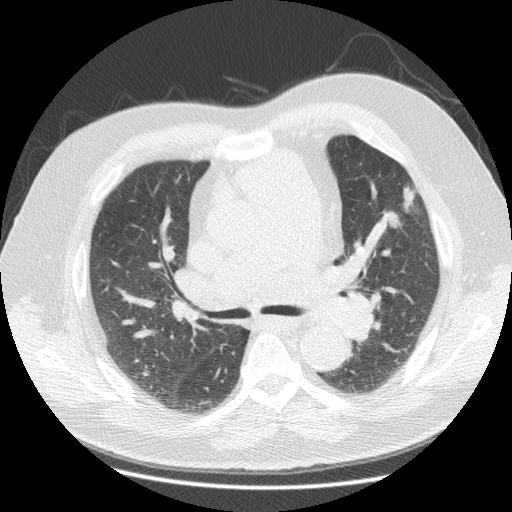
Low-dose screening chest CT, one axial slice. Slice 65 of 116 in the series (ordered by position). Reconstruction kernel STANDARD. 140 kVp. Lung window (W 1500 / L -600 HU). 2.5 mm slice thickness. 512 × 512 image matrix, field of view 390 × 390 mm.
Outlined on this slice (expert manual segmentation):
- lesion 1 (tumor, upper lobe of left lung): bounding box (x1, y1, x2, y2) in pixels: (385, 186, 416, 228)